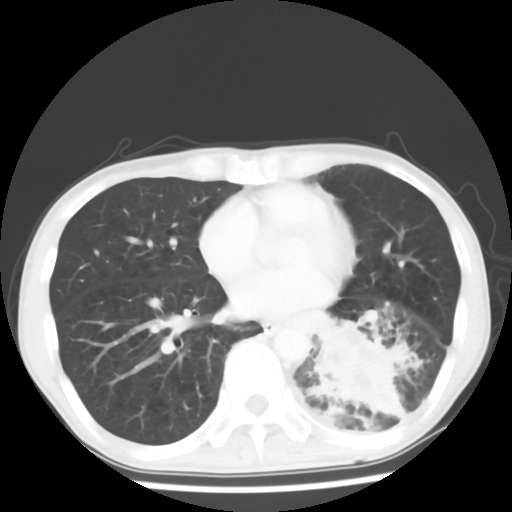
Chest CT, one axial slice. Slice 25 of 64 in the series (ordered by position). Lung window (W 1500 / L -600 HU). 5 mm slice thickness. 512 × 512 image matrix, field of view 313 × 313 mm. Patient: male, 68 years. Case-level facts recorded for this patient, not image findings: clinical TNM (as recorded): T4 N0 M0.
Structures marked on this image (bounding box drawn by a radiologist):
- lung tumour (recorded histology: squamous cell carcinoma): bounding box [x1, y1, x2, y2] px = [301, 312, 416, 429]